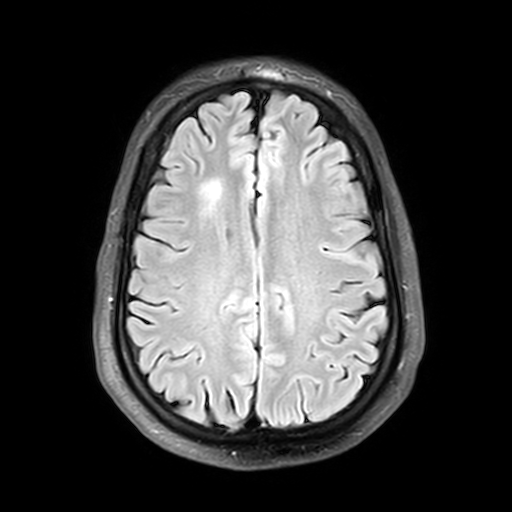
Brain MRI from a brain-tumour surgery series, one axial slice. Slice 14 of 42 in the series (ordered by position). T2 FLAIR. 512 × 512 image matrix, field of view 240 × 240 mm. From the clinical record (not read from this slice): histopathology: Astrocytoma; WHO grade: 2; IDH mutation: yes; tumour location: Right Insular.
Structures marked on this image (expert manual segmentation):
- tumour: bounding box <201,180,222,210> (left, top, right, bottom; pixels)